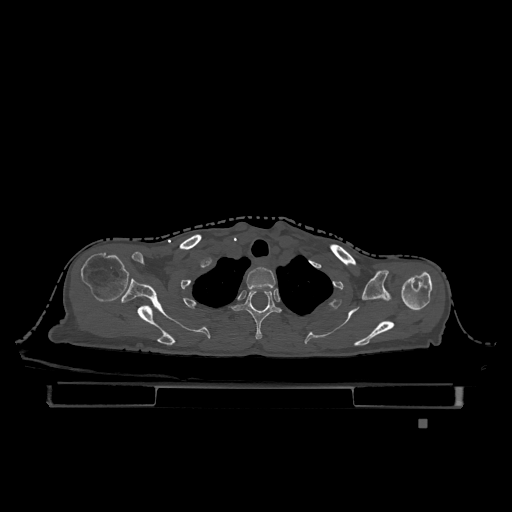
CT including the spine, one axial slice; bone window (W 1800 / L 400 HU); 0.5 mm slice thickness; 512 × 512 image matrix, field of view 500 × 500 mm. Female patient, age 74 years. Case-level facts recorded for this patient, not image findings: primary cancer: lung.
Outlined on this slice (semi-automatically segmented with operator editing):
- T1 vertebra: bounding box <246,267,276,290> (left, top, right, bottom; pixels)
- T2 vertebra: <232,290,282,339>